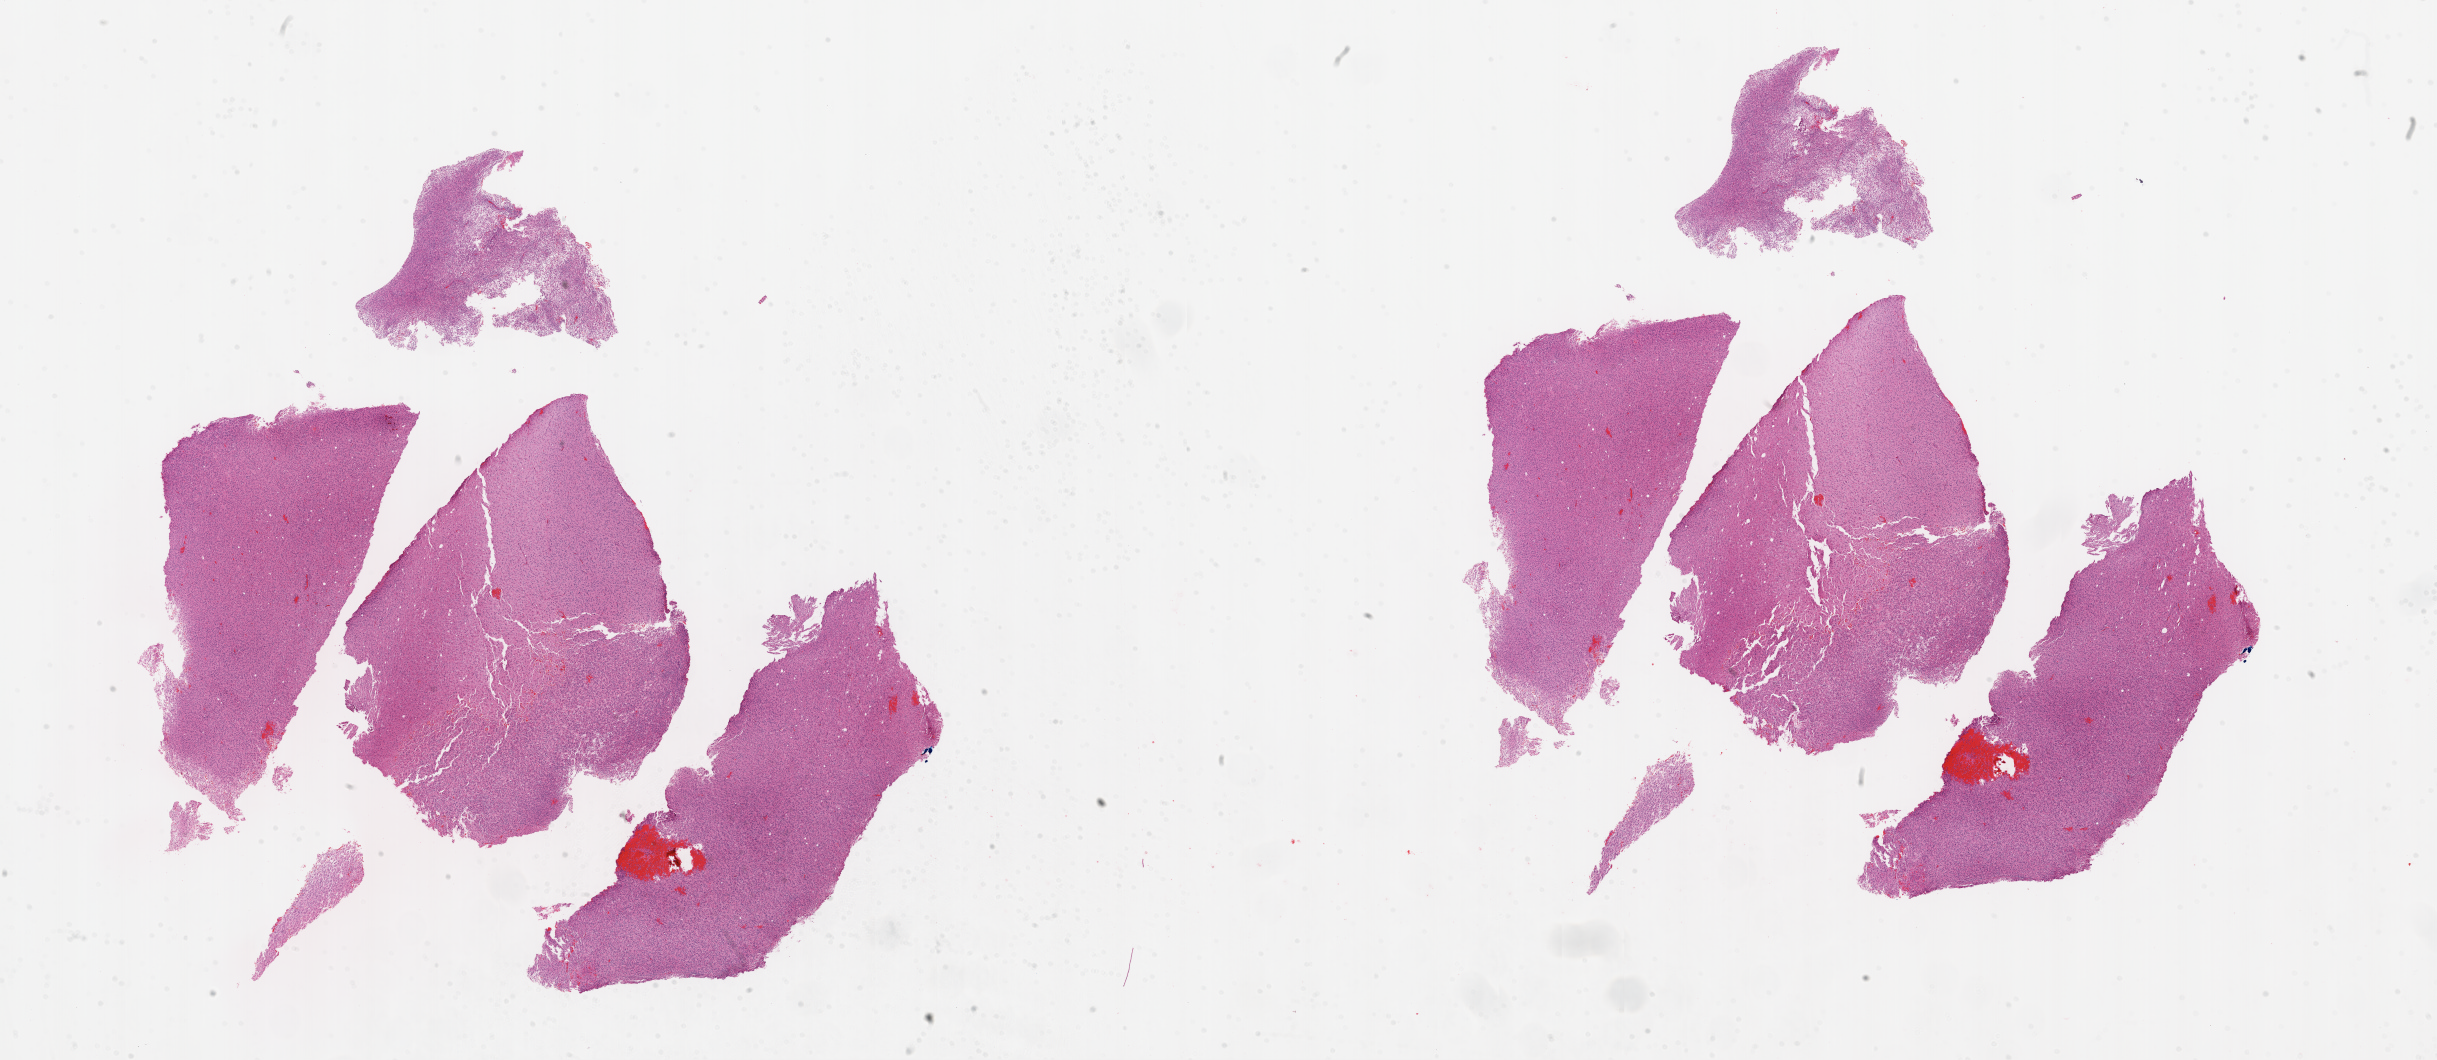
Digitized H&E-stained tissue section (whole slide) — whole scanned area (about 39.1 x 17.0 mm, acquisition: 20x scan) shown as a low-resolution overview. Frozen section from the top of the tissue portion. Primary tumour sample from the brain. Patient: male, age at initial diagnosis 67 years.
Histologic diagnosis: Glioblastoma.